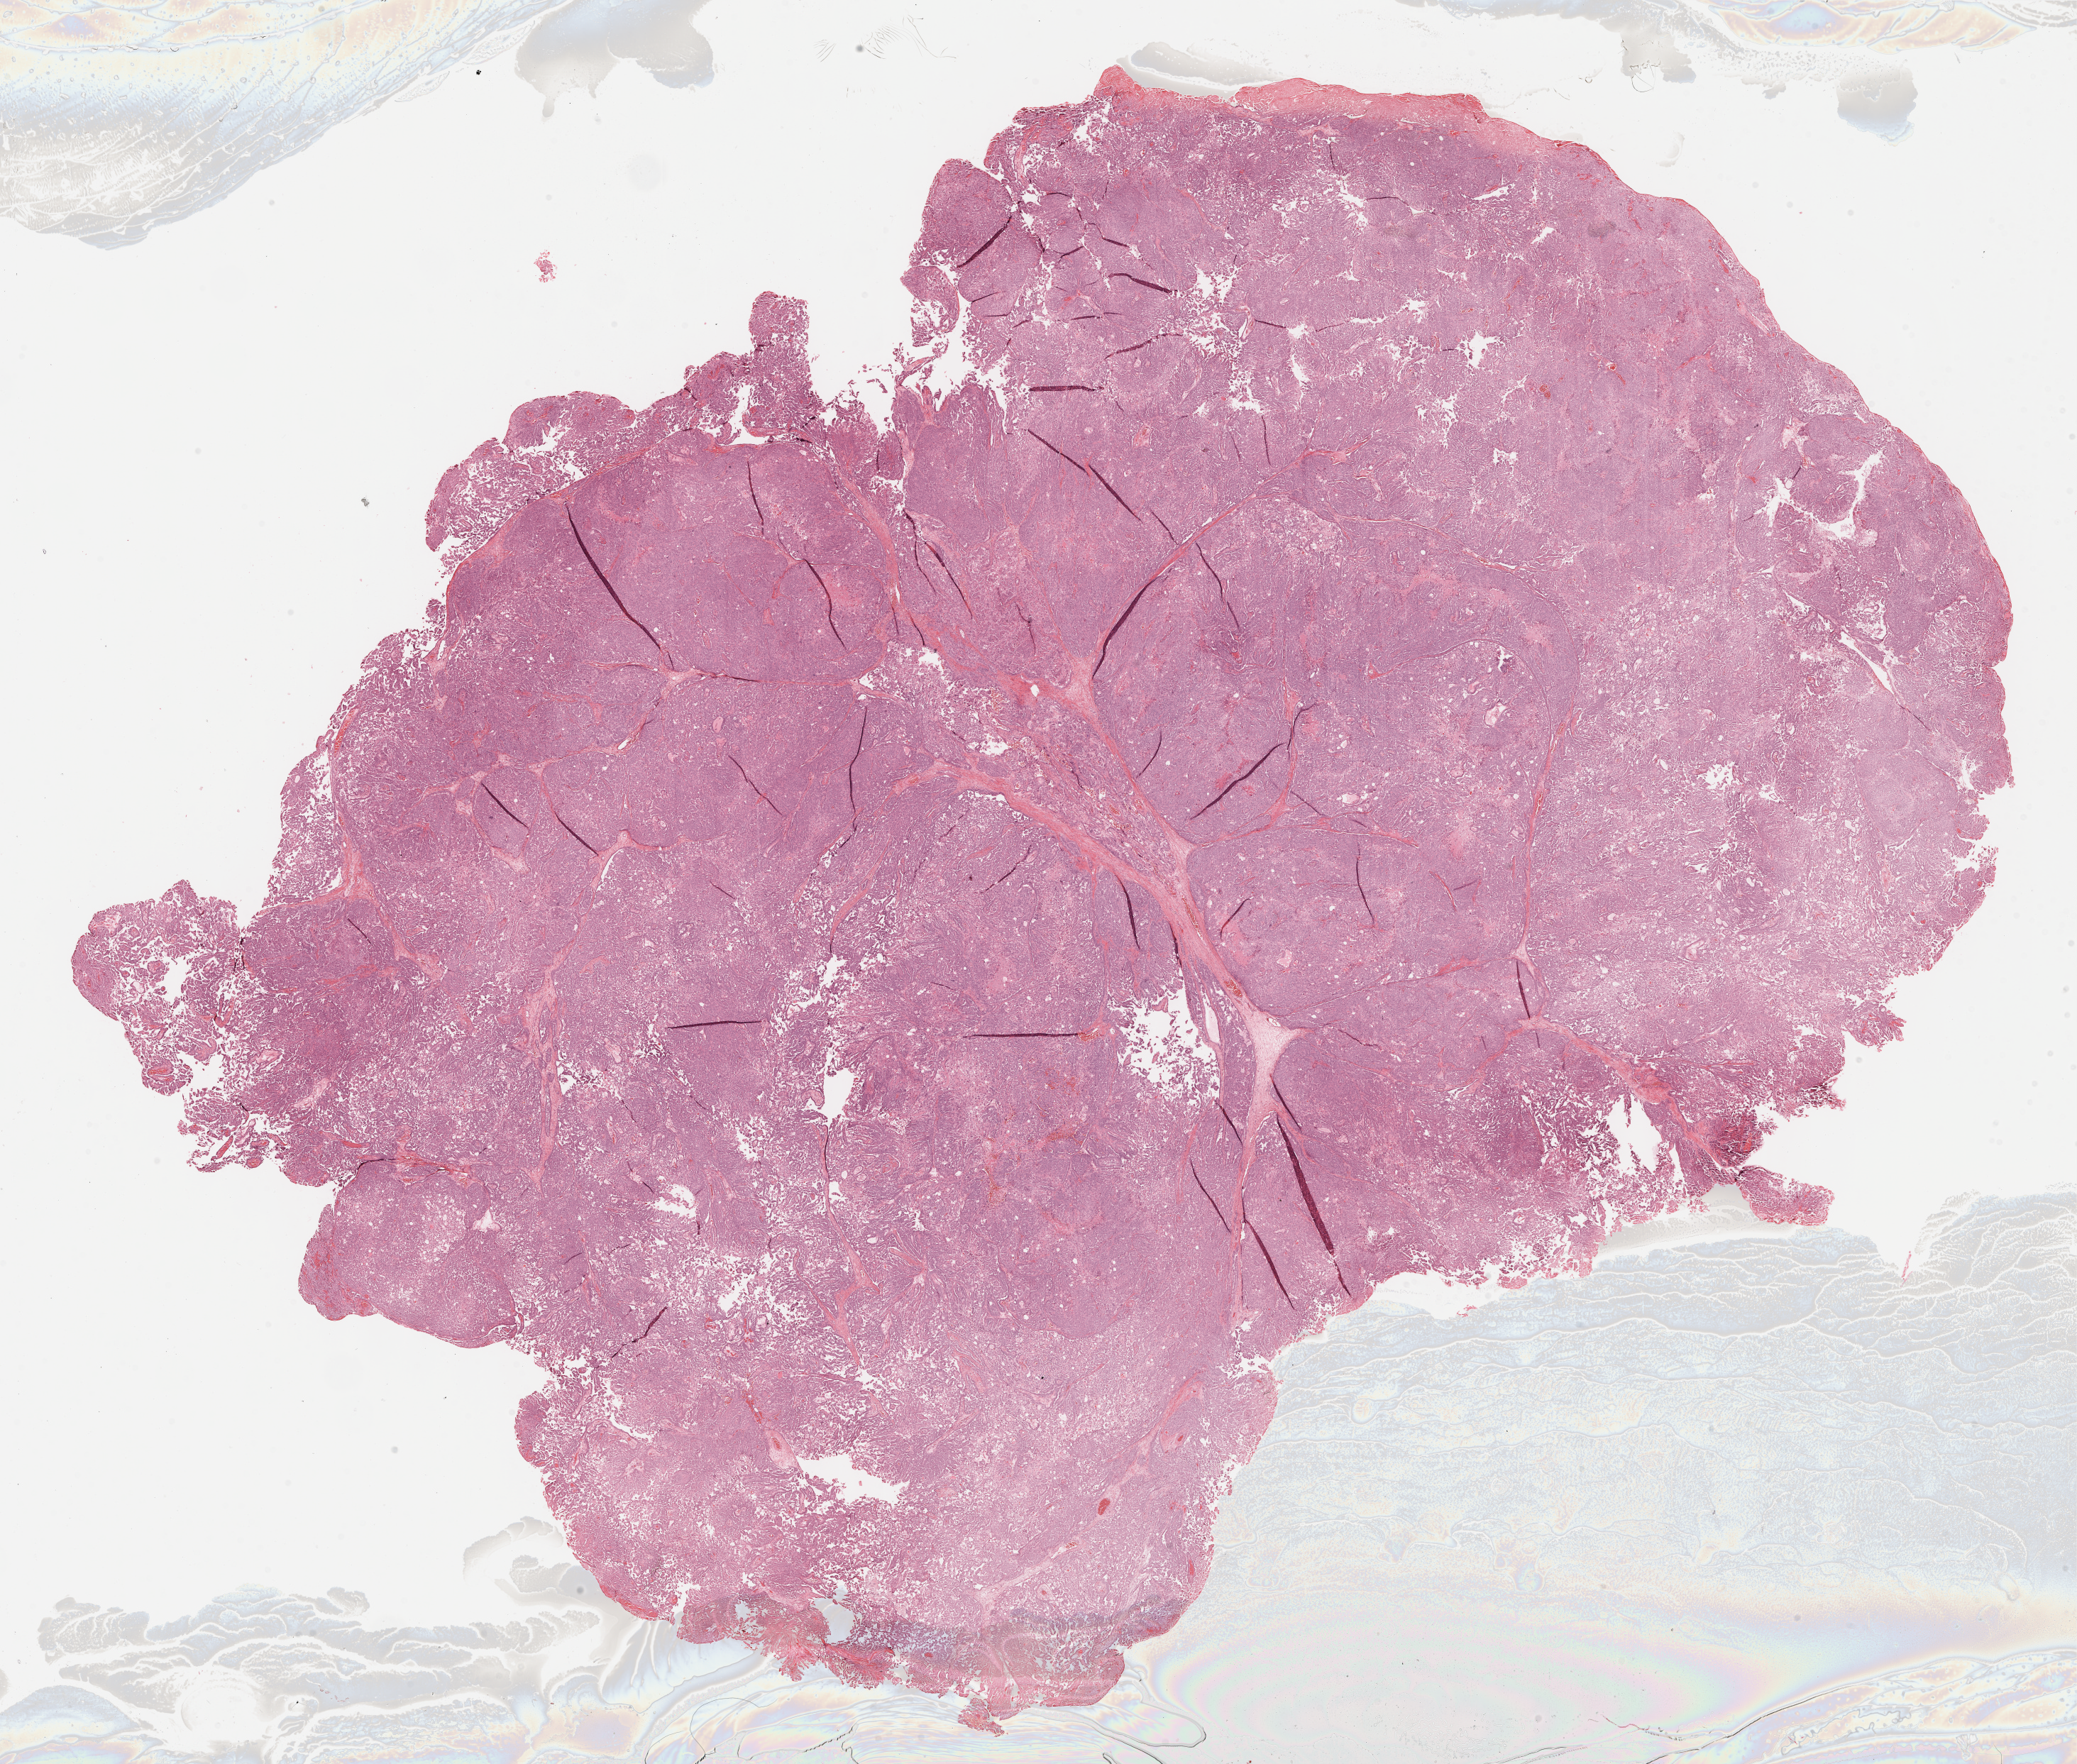
H&E whole-slide image, shown as a low-resolution overview of the whole scanned area (about 23.6 x 20.1 mm). Formalin-fixed paraffin-embedded (FFPE) diagnostic section. Primary tumour sample from the ovary. Female patient; age at initial diagnosis 42 years. Histologic grade: G3 (poorly differentiated).
Laterality: bilateral. FIGO stage: IV. Diagnosis: Serous cystadenocarcinoma, NOS.